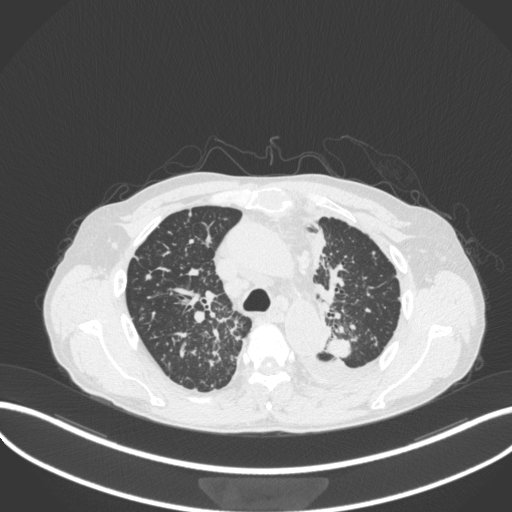
Chest CT, one axial slice. Position 253 of 319 along the scan axis. Reconstruction kernel B31f. 120 kVp. Lung window (W 1500 / L -600 HU). 512 × 512 image matrix, field of view 400 × 400 mm. Male patient, age 58 years. Case-level facts recorded for this patient, not image findings: clinical TNM (as recorded): T1c N3 M1.
Annotated regions visible in this slice (rectangle marked by the reading radiologist):
- lung tumour (recorded histology: adenocarcinoma): bounding box <321,335,357,360> (left, top, right, bottom; pixels)